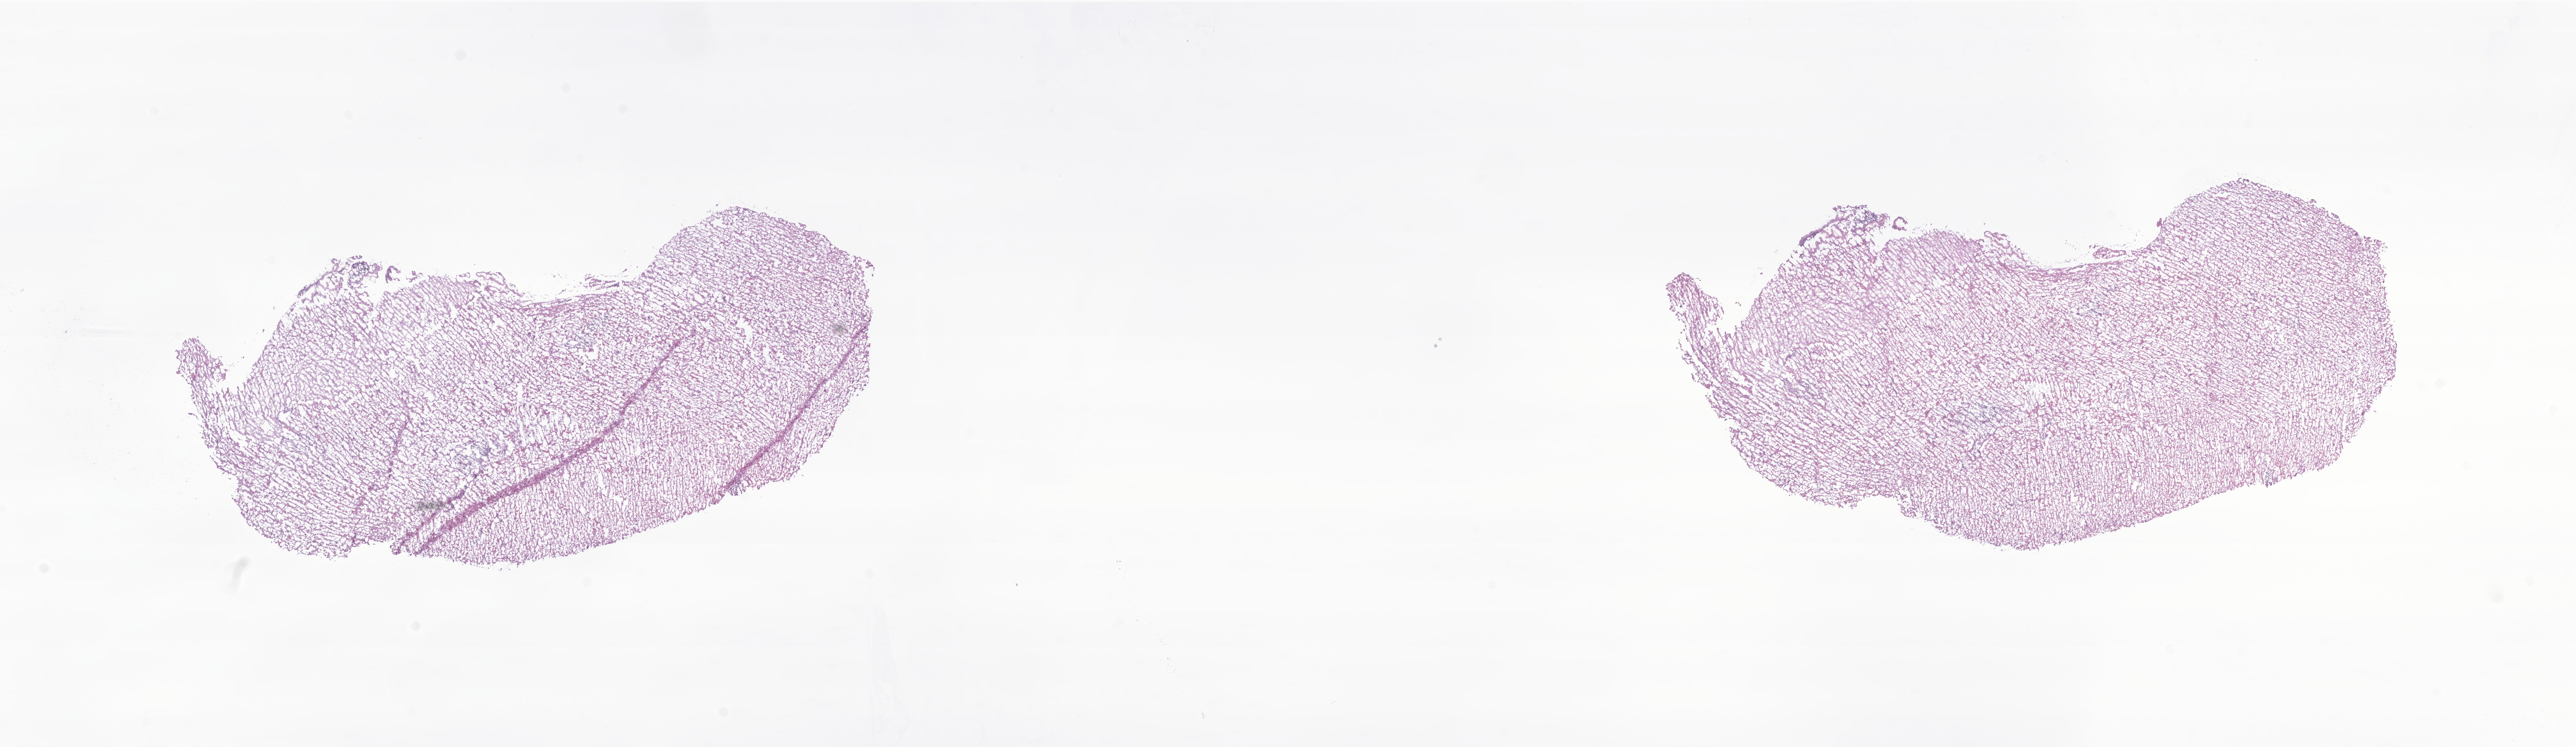
H&E whole-slide image of tumor tissue from the brain — a low-resolution overview of the entire scanned area, about 26.7 x 7.7 mm, cryosection (OCT / tissue freezing medium). Patient male; age 197 months (16 years 5 months).
Recorded diagnosis: Pilocytic astrocytoma.